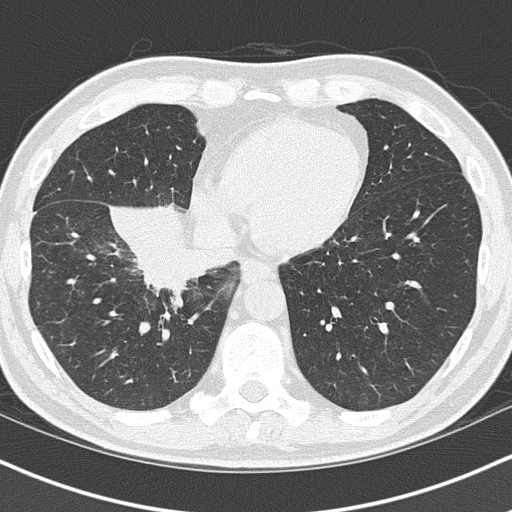
Low-dose screening chest CT, one axial slice; position 39 of 151 along the scan axis; reconstruction kernel B50f; 120 kVp; lung window (W 1500 / L -600 HU); 2 mm slice thickness; 512 × 512 image matrix, field of view 320 × 320 mm.
Outlined on this slice (outlined manually by an expert reader):
- lesion 1 (tumor, hilum of right lung): bounding box <140,237,209,289> (left, top, right, bottom; pixels)